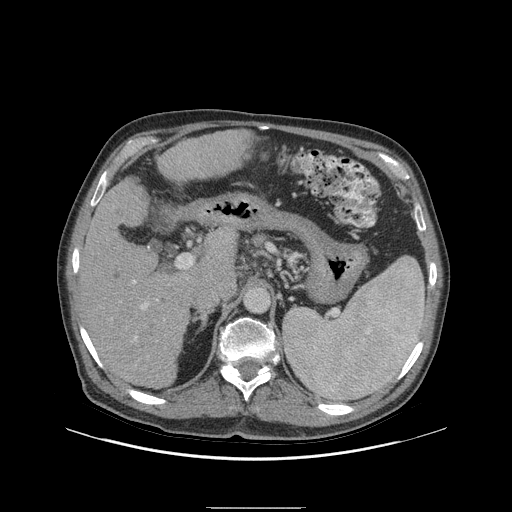
Contrast-enhanced abdominal CT (liver protocol), one axial slice. Slice 56 of 105 in the series (ordered by position). Reconstruction kernel STANDARD. Soft-tissue window (W 400 / L 40 HU). 2.5 mm slice thickness. 512 × 512 image matrix, field of view 440 × 440 mm. Case-level facts recorded for this patient, not image findings: diagnosis: hepatocellular carcinoma (patient treated with transarterial chemoembolisation; whether this scan precedes or follows treatment is not stated here); TNM stage (as recorded): Stage-I; Child-Pugh class: A; tumour size: 5.1 cm.
Outlined on this slice (semi-automatically segmented with operator editing):
- liver parenchyma outside the tumour (the mass and vessels are separate outlines, so this box may not span the whole liver): box from (x=76, y=140) to (x=208, y=388) px
- liver vessels: (x=133, y=280)–(x=148, y=340)